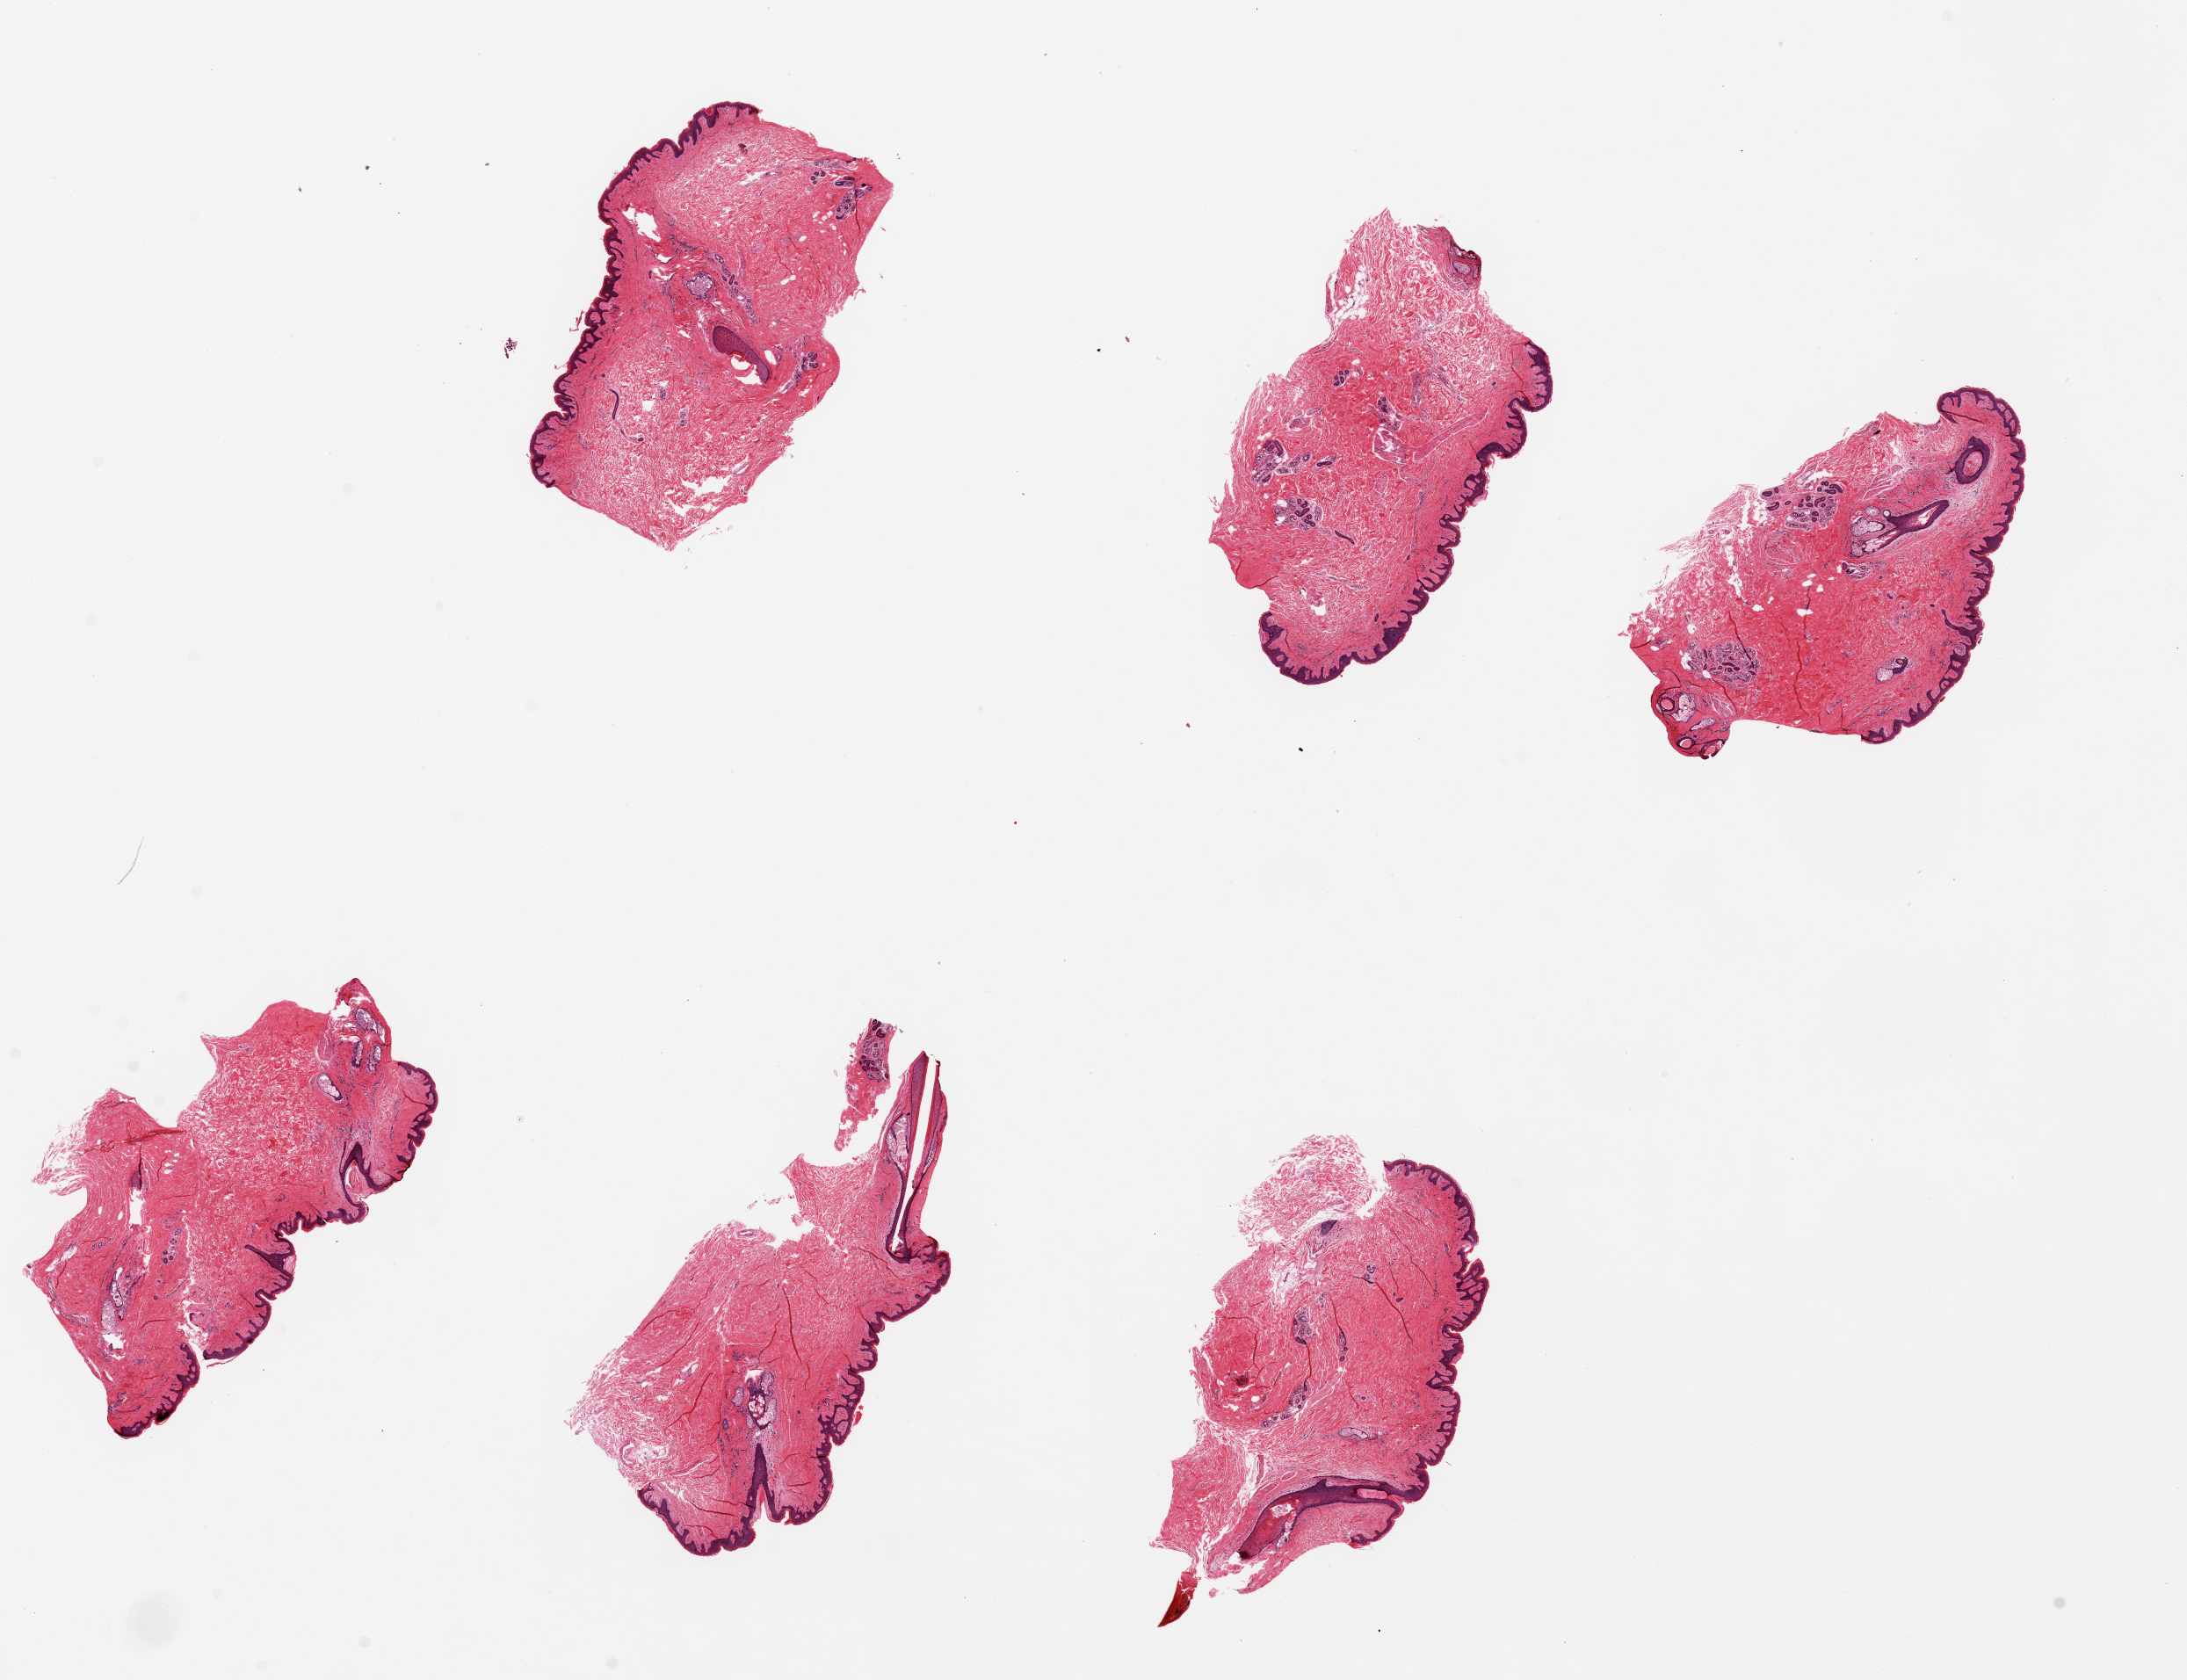
H&E whole-slide image, shown as a low-resolution overview of the whole scanned area (about 19.7 x 15.1 mm, from a 20x scan); PAXgene-fixed, paraffin-embedded tissue; section of skin of suprapubic region (target tissue); tissue donor sample. Donor sex: male.
Review note (as recorded): 6 pieces, up to 5x2mm; no subcutaneous adipose, good dissection.